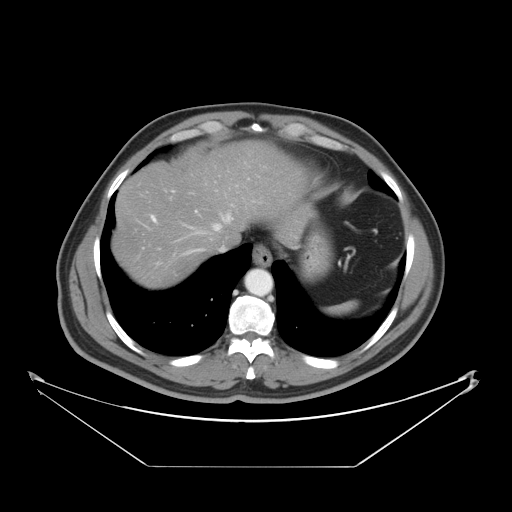
Contrast-enhanced abdominal CT, one axial slice; slice 38 of 46 in the series (ordered by position); intravenous contrast given; soft-tissue window (W 400 / L 40 HU); 5 mm slice thickness; 512 × 512 image matrix. Male patient, age 57 years. Case-level facts recorded for this patient, not image findings: diagnosis: colorectal cancer liver metastases, imaged before liver resection; multiple liver metastases: no.
Annotated regions visible in this slice (expert manual segmentation):
- hepatic veins: bounding box [x1, y1, x2, y2] px = [186, 205, 233, 254]
- liver: [115, 140, 303, 287]
- planned liver remnant (the part of the liver to remain after resection): [115, 140, 304, 277]
- portal vein (with intrahepatic branches): [151, 215, 157, 222]